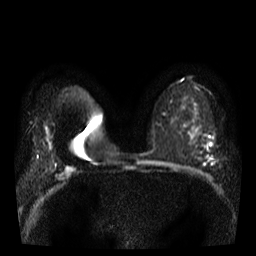
Breast MRI, one axial slice; position 22 of 38 along the scan axis; diffusion-weighted series; image 2 of 4 stored at this slice position (different b-values; order by instance number); 3 T; 5 mm slice thickness; 256 × 256 image matrix, field of view 320 × 320 mm. Female patient.
Annotated regions visible in this slice (manually delineated by an expert):
- tumour on diffusion-weighted imaging: bounding box [x1, y1, x2, y2] px = [209, 143, 212, 146]